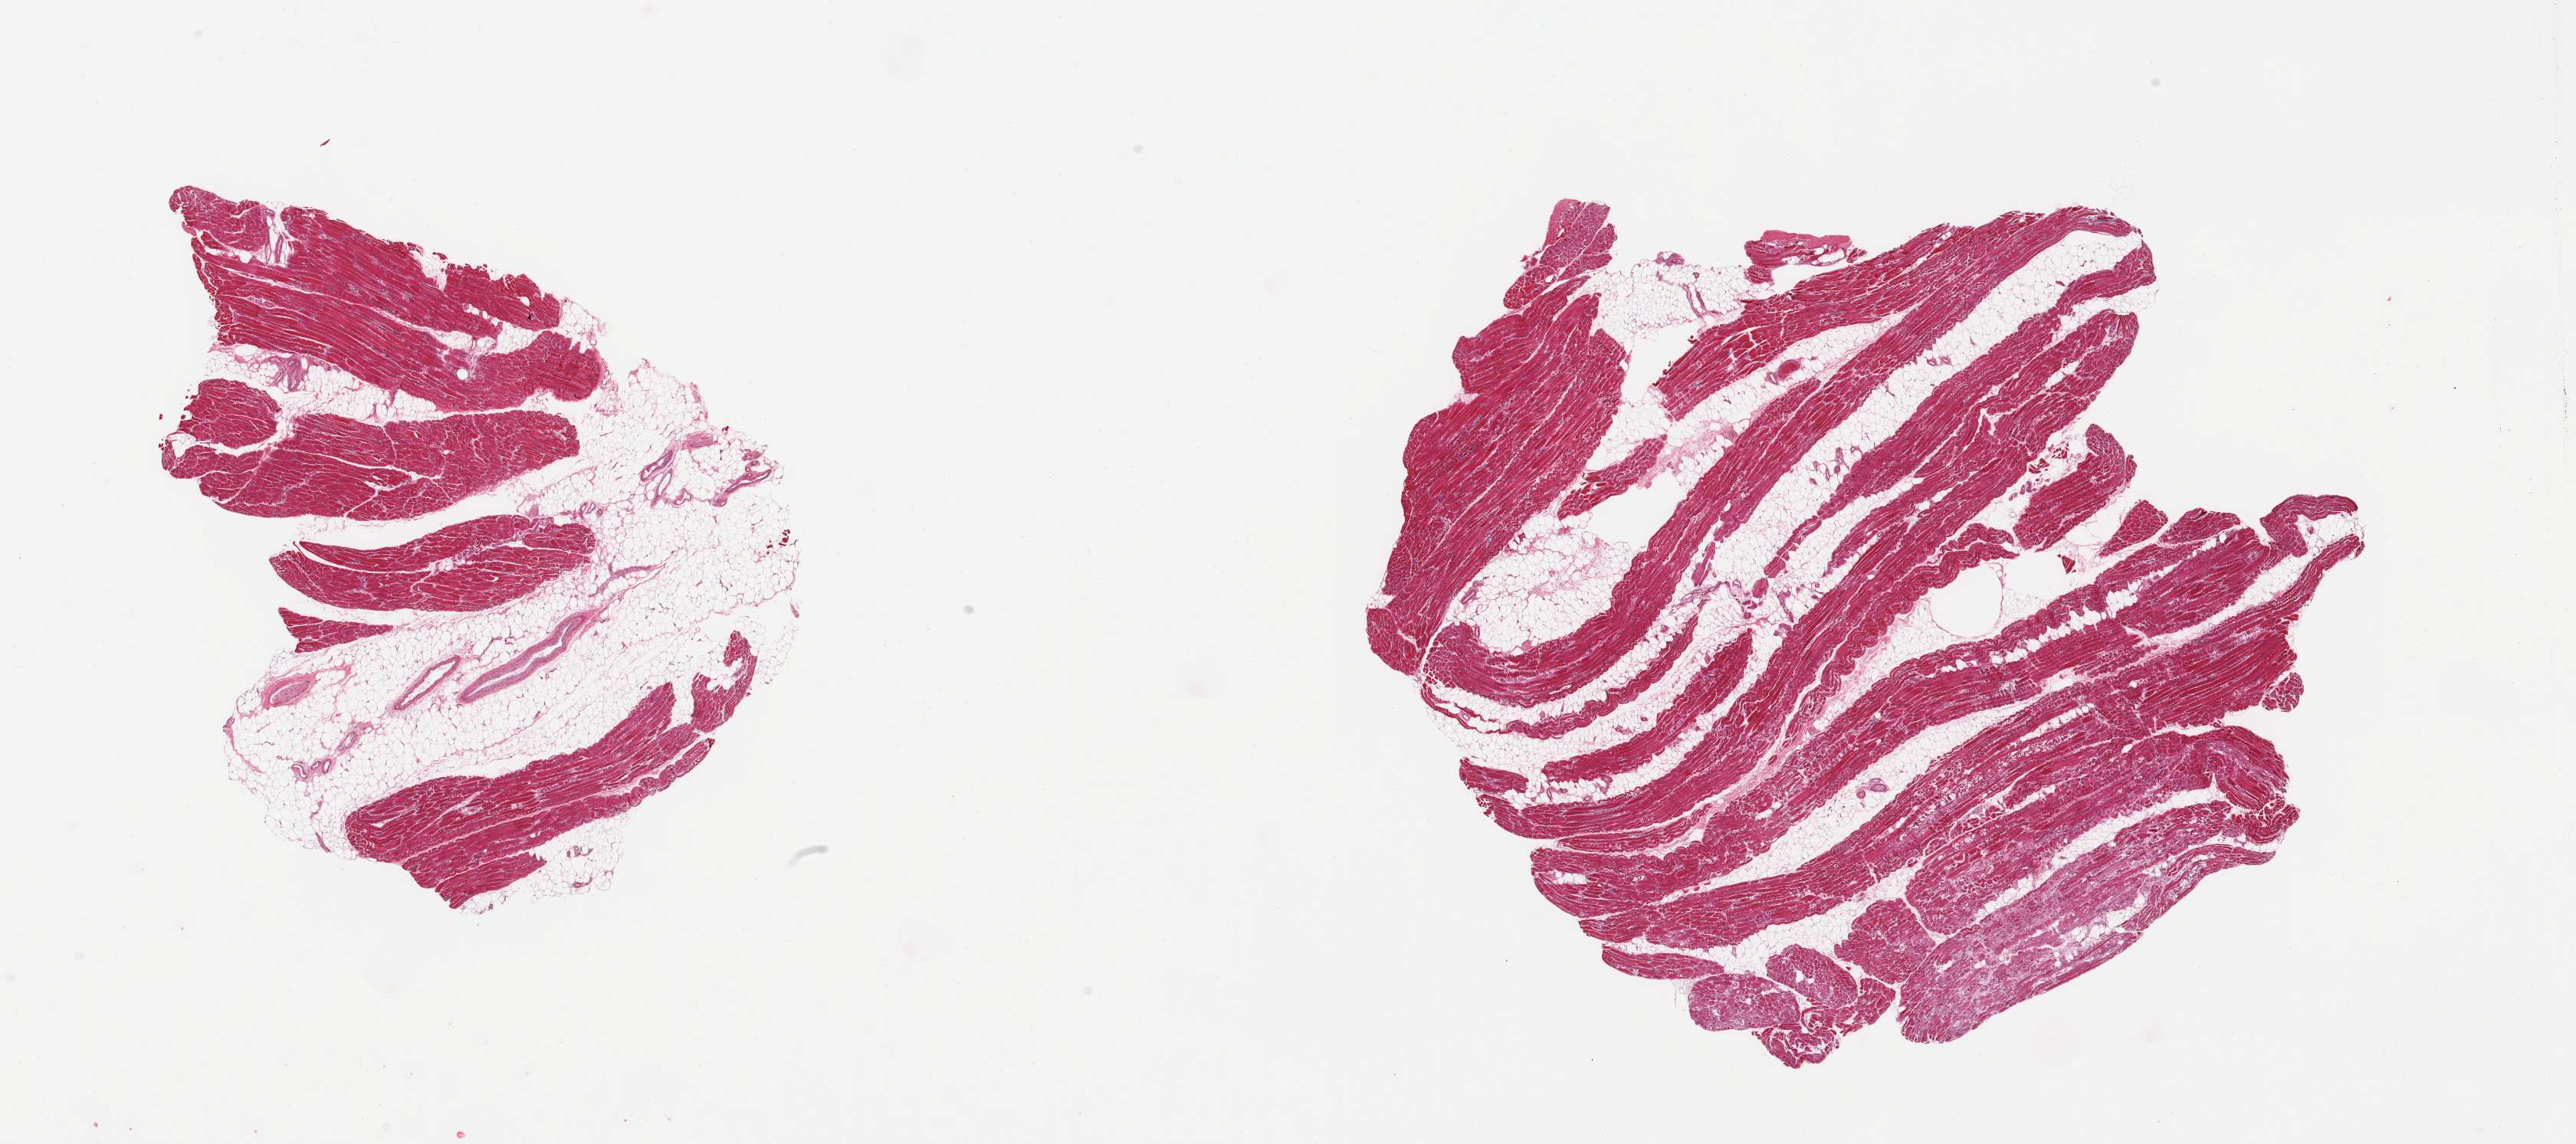
Digitized haematoxylin and eosin-stained section — a low-resolution overview of the entire scanned area, about 26.6 x 11.8 mm, PAXgene-fixed, paraffin-embedded tissue, section of skeletal muscle (target tissue), tissue donor sample. Female donor.
Pathologist's review note for this sample: 2 pieces; include 30 and 50% mostly internal fat, some atrophy, degeneration of fibers.